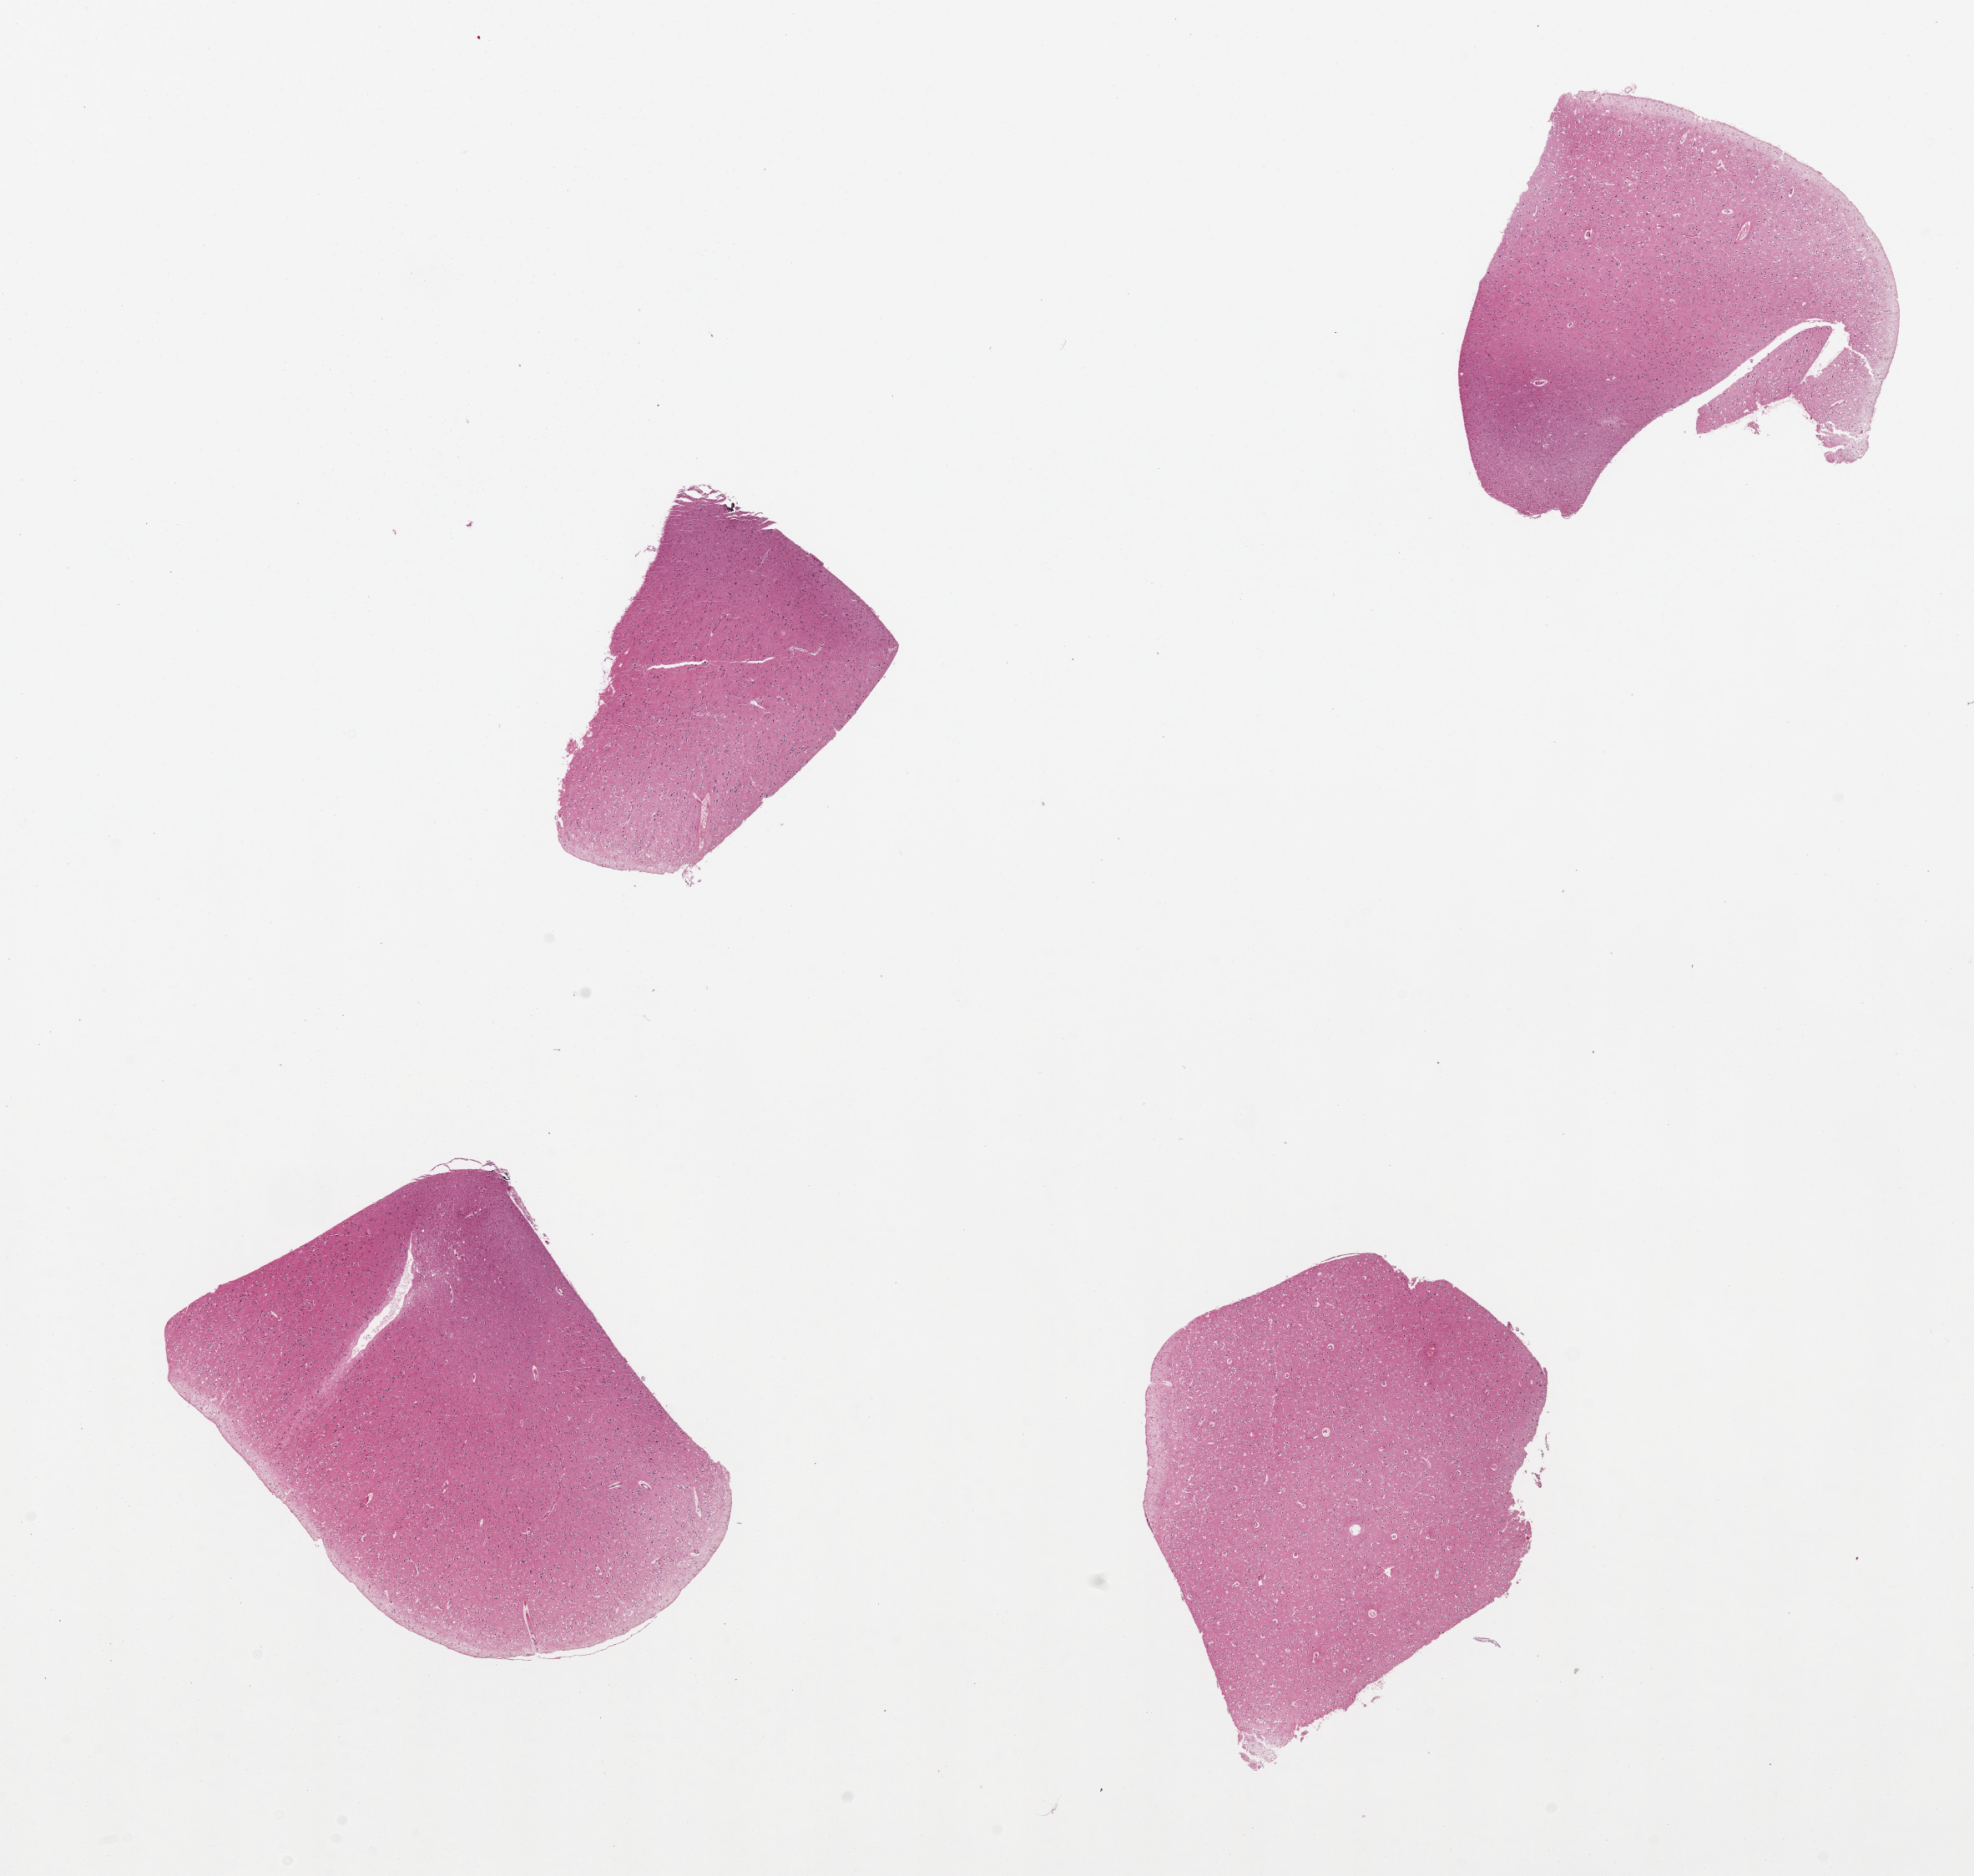
Haematoxylin and eosin whole-slide image — a low-resolution overview of the entire scanned area, about 18.7 x 17.8 mm (from a 20x scan), PAXgene-fixed paraffin-embedded (PFPE) section, sampled site (target tissue): cerebral cortex, donor tissue sample. Donor sex: male.
Reviewer comment on this tissue sample: 4 pieces.